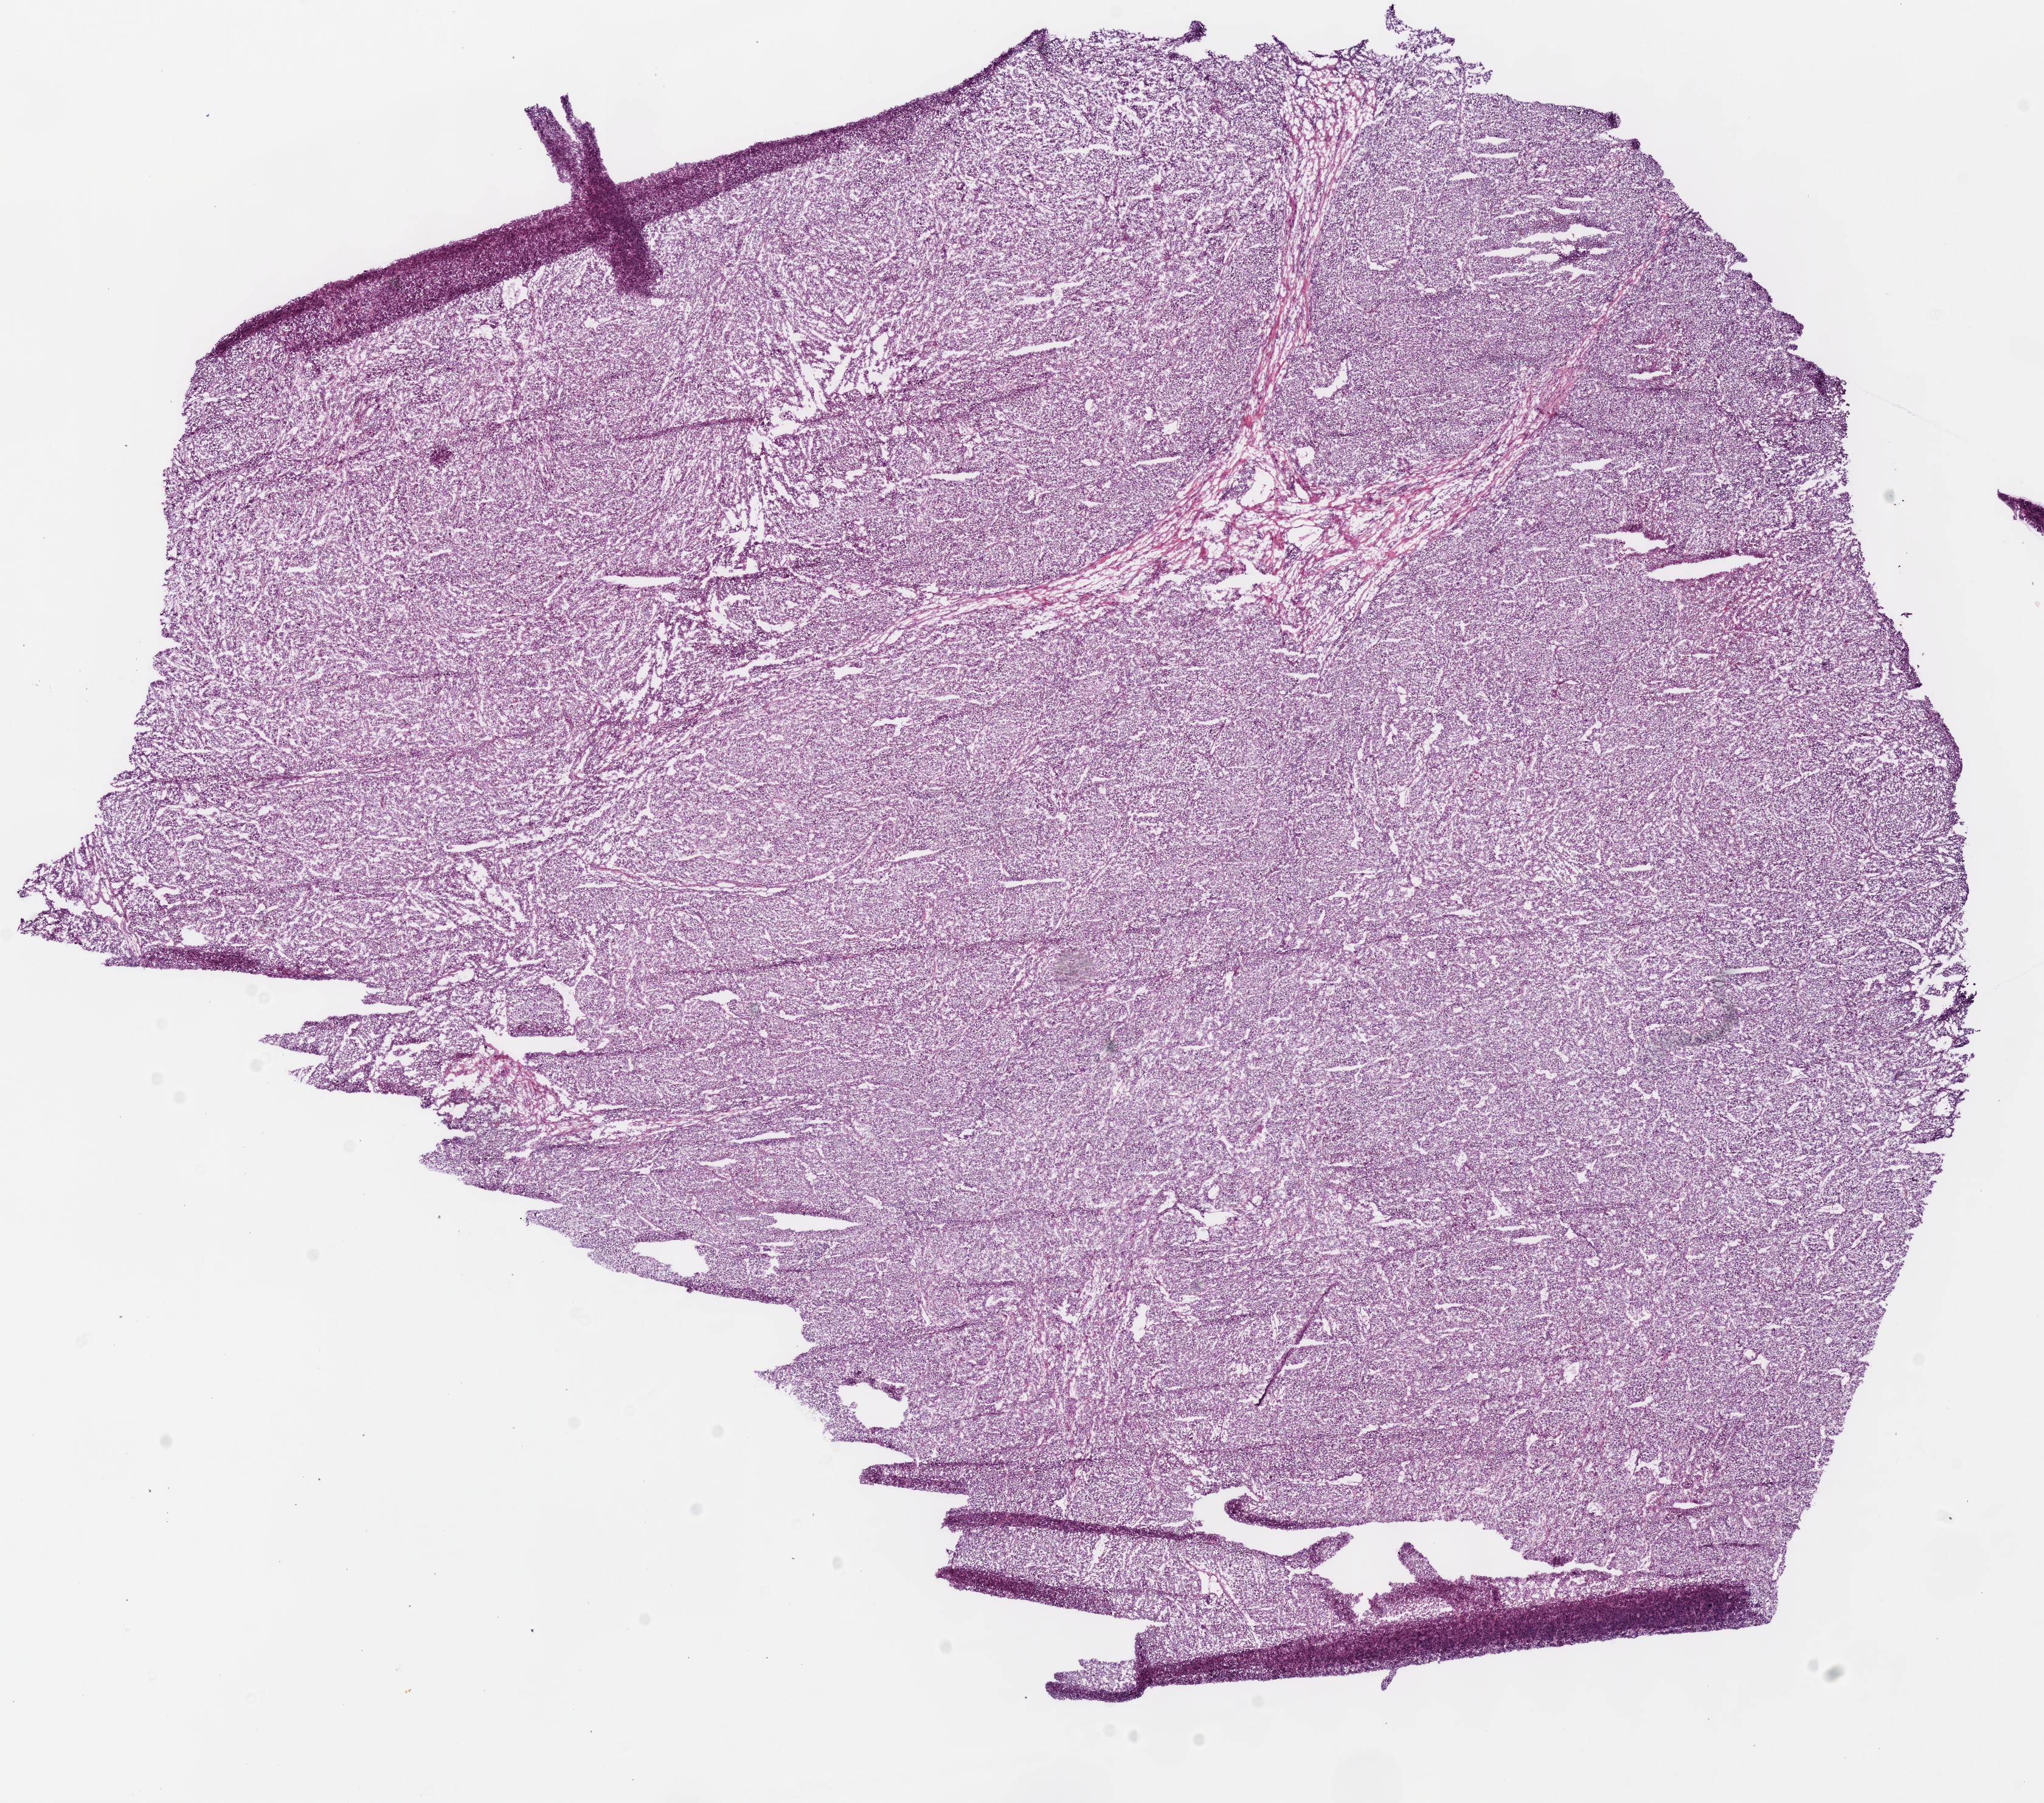
Digitized H&E tissue section (whole slide), whole scanned area (about 13.2 x 11.7 mm, acquisition: 40x scan) shown as a low-resolution overview, frozen section from the bottom of the tissue portion, sample: primary tumour, lung. Male, age 70 years at initial diagnosis. Composition of this section per pathologist review: tumour cells 100%, tumour nuclei 65%, normal cells 0%, stromal cells 0%, necrosis 0%. Inflammatory infiltration, as recorded: lymphocyte infiltration 5%, monocyte infiltration 5%, neutrophil infiltration 20%.
Histologic diagnosis: Adenocarcinoma, NOS (lower lobe, lung). AJCC pathologic stage: IIA (7th edition).